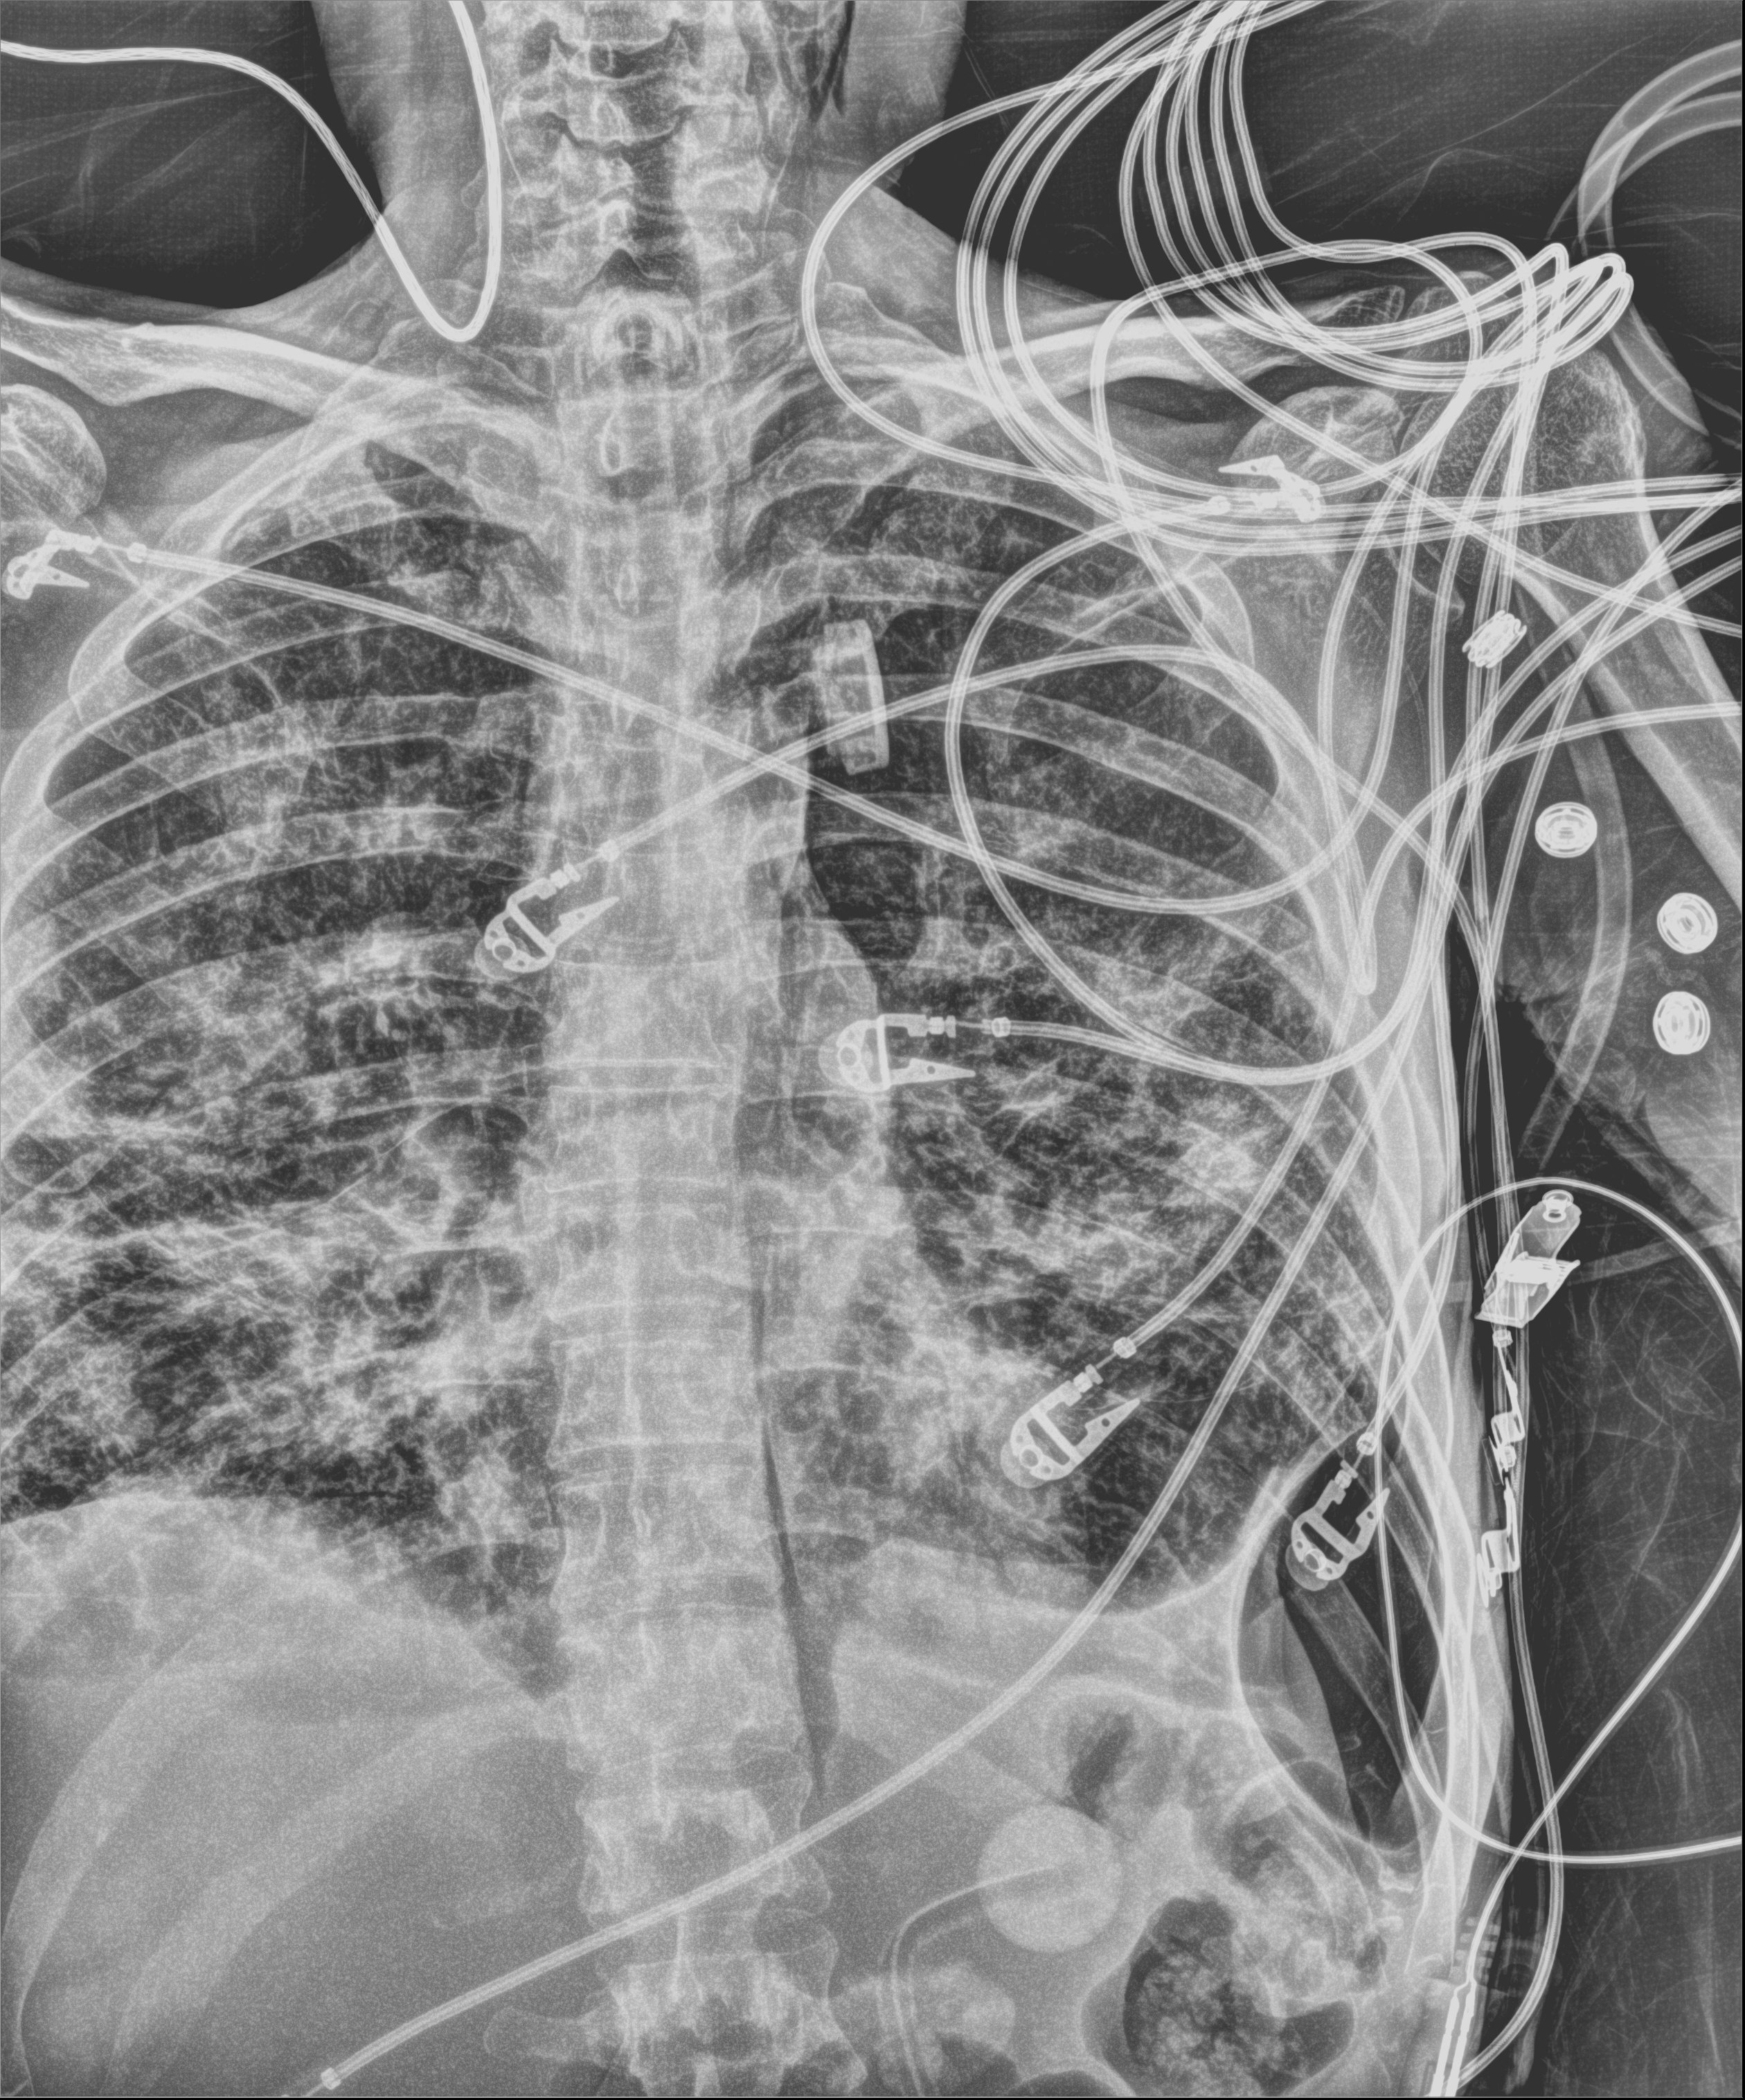
Chest X-ray; anteroposterior (AP) projection. Male patient hospitalised with COVID-19, age 18–59 years.
Admission-level facts for this patient (not findings on this image; timing relative to this image not recorded):
- length of hospital stay: 96 days
- admitted to intensive care during this hospital stay: yes